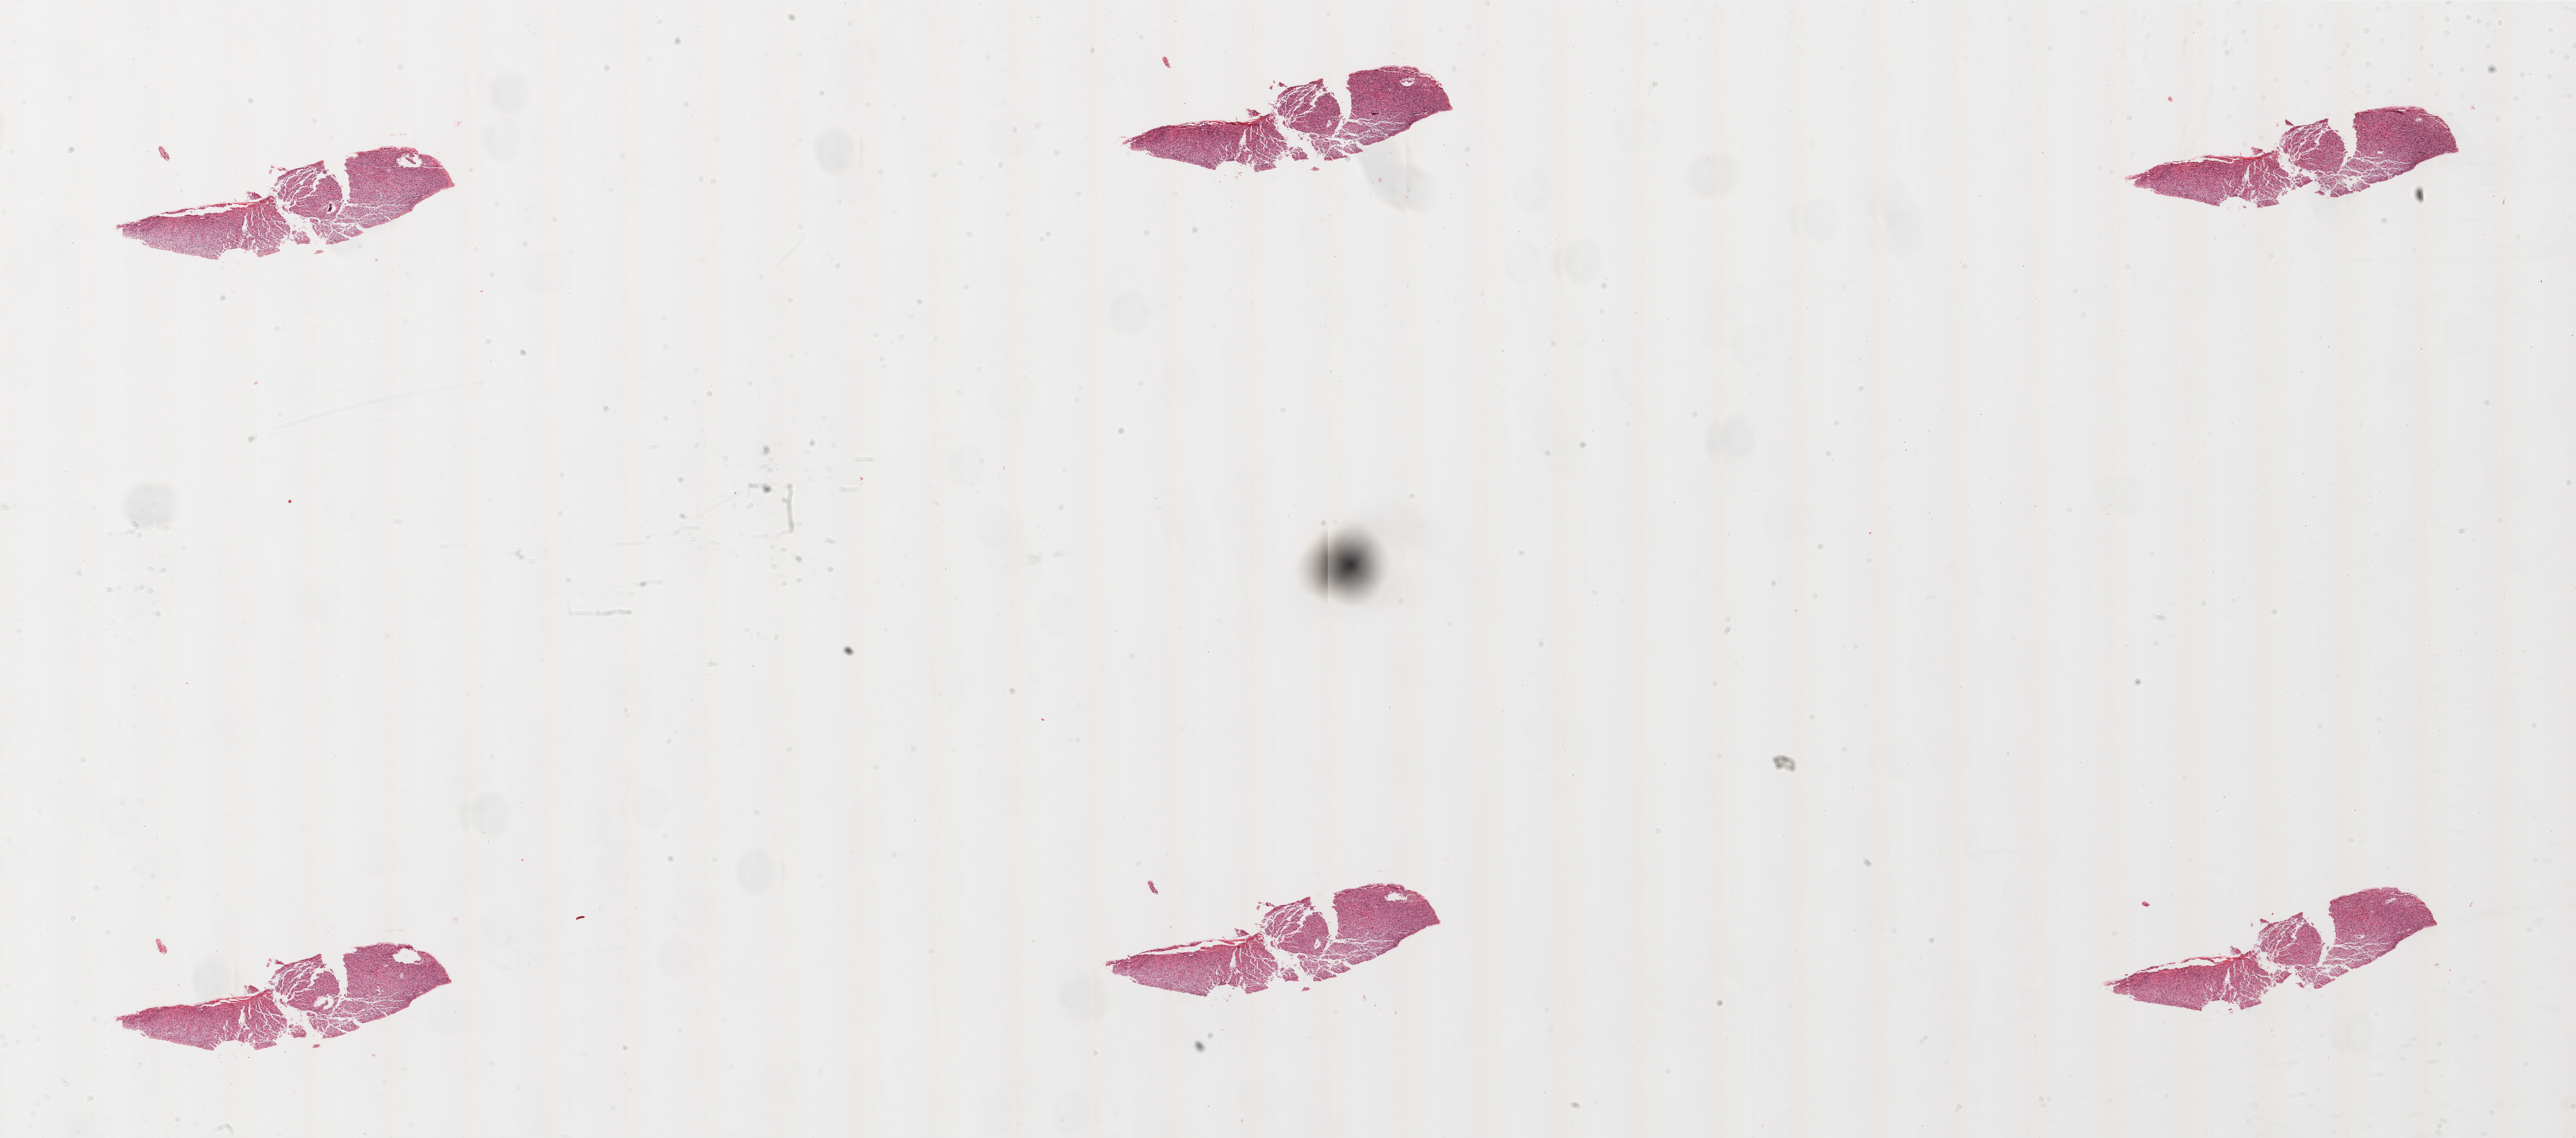
Digitized Hematoxylin and eosin (H&E) stained tissue section (whole slide), whole scanned area (about 33.0 x 14.6 mm, slide scanned at 20x) shown as a low-resolution overview, formalin-fixed paraffin-embedded (FFPE) diagnostic section, brain, primary tumour sample. Female, age 63 years at initial diagnosis.
Pathologic diagnosis: Glioblastoma.